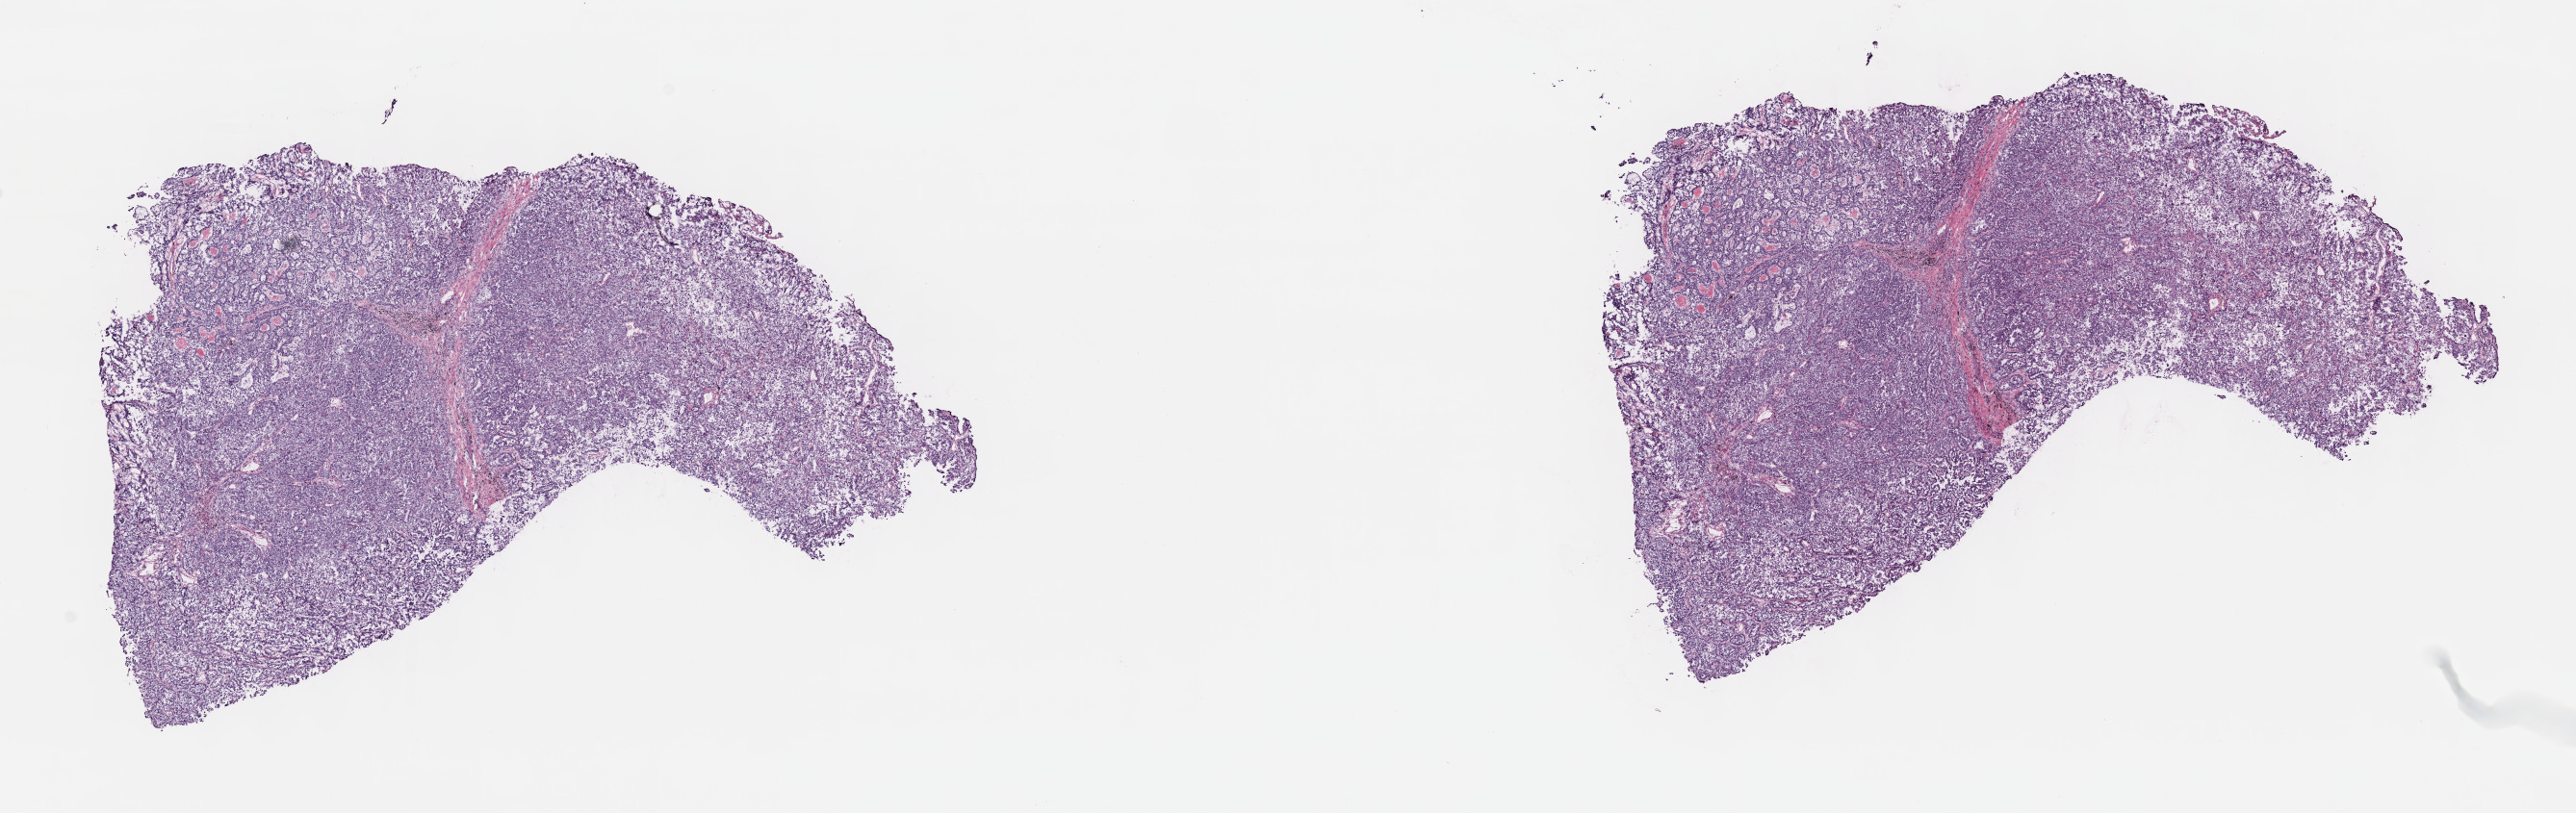
H&E-stained whole-slide image — whole scanned area (about 21.6 x 6.8 mm, from a 40x scan) shown as a low-resolution overview, frozen section from the top of the tissue portion, sample: primary tumour, lung. Male patient; age at initial diagnosis 69 years. Pathologist review of this section (percent, as recorded): tumour cells 80%, tumour nuclei 80%, normal cells 0%, stromal cells 10%, necrosis 10%. Infiltration values recorded for this section: lymphocyte infiltration 40%, monocyte infiltration 20%, neutrophil infiltration 20%.
Pathologic diagnosis: Adenocarcinoma, NOS. AJCC pathologic stage: IIA (7th edition).